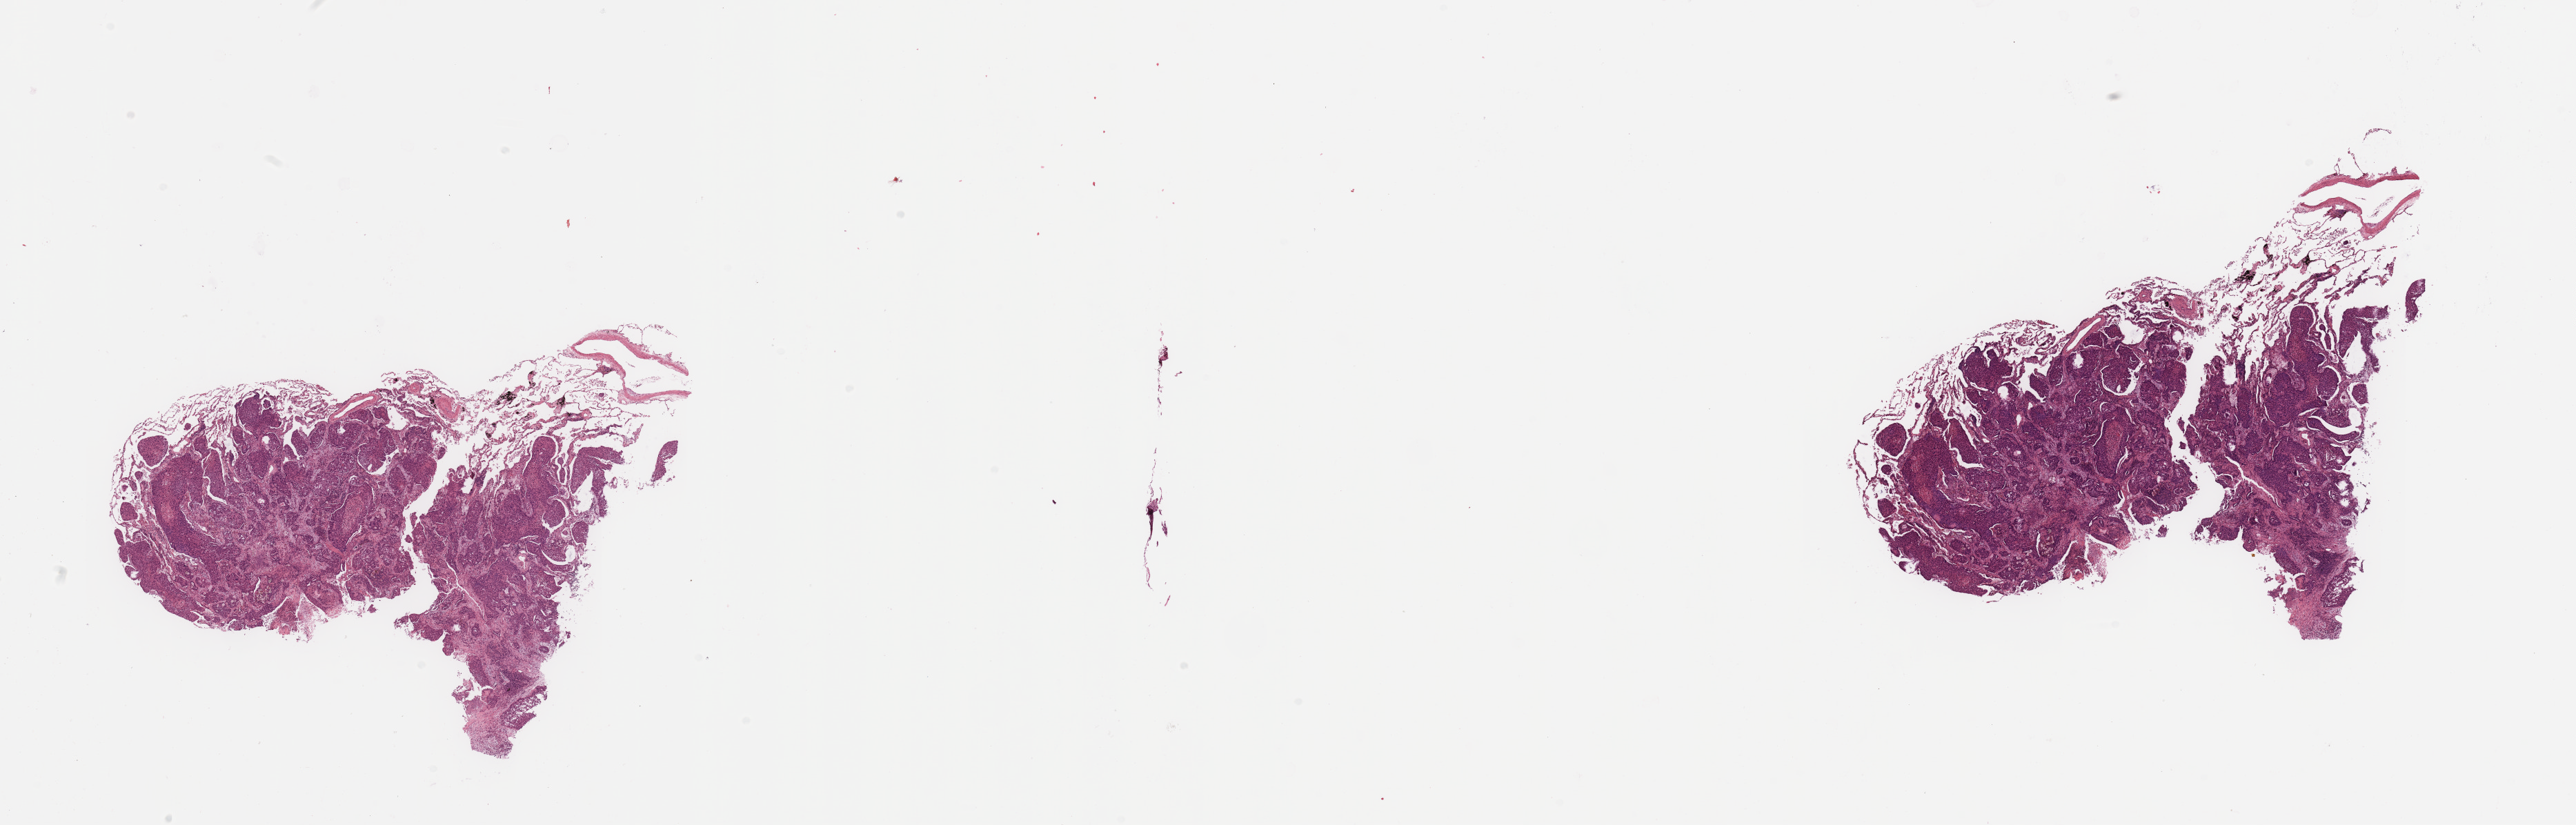
Digitized H&E tissue section (whole slide), whole scanned area (about 29.5 x 9.5 mm, slide scanned at 20x) shown as a low-resolution overview. Tumour tissue sample, sampled site: lung. Patient: male, age 67 years. Histologic grade: G3 (poorly differentiated). Slide review estimates, as recorded: tumour nuclei 70%, necrosis 5%.
* primary tumour site (as recorded): left upper lobe
* histologic diagnosis: Squamous cell carcinoma, NOS
* AJCC pathologic stage: IIIA